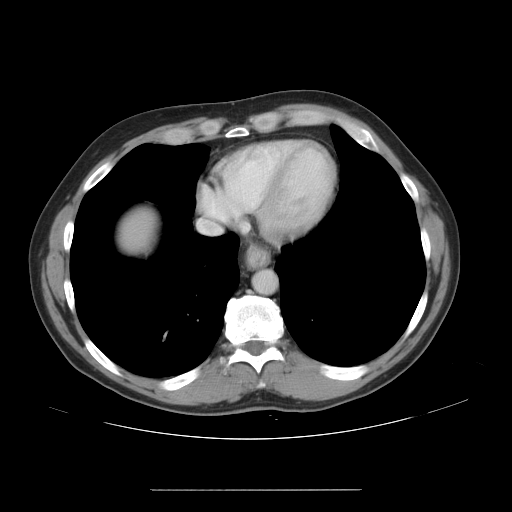
Contrast-enhanced abdominal CT, one axial slice. Slice 42 of 48 in the series (ordered by position). Reconstruction kernel STANDARD. 120 kVp. Intravenous contrast given. Soft-tissue window (W 400 / L 40 HU). 5 mm slice thickness. 512 × 512 image matrix. Male patient, age 56 years. Case-level facts recorded for this patient, not image findings: diagnosis: colorectal cancer liver metastases, imaged before liver resection; multiple liver metastases: yes; largest metastasis: 1.8 cm.
Annotated regions visible in this slice (manually delineated by an expert):
- hepatic veins: box from (x=200, y=222) to (x=219, y=232) px
- liver: (x=128, y=219)–(x=144, y=245)
- planned liver remnant (the part of the liver to remain after resection): (x=128, y=218)–(x=144, y=245)